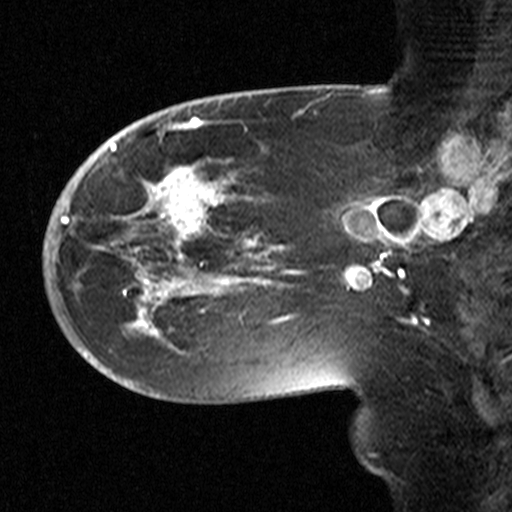
Breast MRI (dynamic contrast-enhanced), one sagittal slice; dynamic contrast-enhanced study with each time point stored as its own series, time point 2 of 3 at this slice position (early post-contrast, ordered by acquisition time); 1.5 T; TE 4.5 ms, TR 11 ms; 3.27 mm slice thickness; 512 × 512 image matrix, field of view 200 × 200 mm. Patient: female, 53 years. Case-level facts recorded for this patient, not image findings: setting: breast cancer imaged before/during neoadjuvant chemotherapy; receptor status: HR-positive, HER2-negative.
Annotated regions visible in this slice (semi-automatic segmentation, software-assisted and operator-edited):
- analysis volume of interest (the breast-tissue region the enhancement analysis was run in; not a lesion): bounding box (x1, y1, x2, y2) in pixels: (58, 154, 311, 367)
- tumour enhancement mask (voxels above the 90 % enhancement threshold inside the analysis volume of interest): (61, 163, 303, 335)